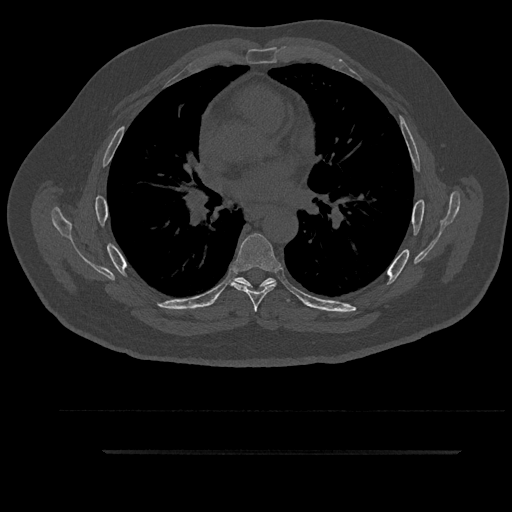
CT including the spine, one axial slice; slice 564 of 797 in the series (ordered by position); reconstruction kernel Br40s/3; 120 kVp; bone window (W 1800 / L 400 HU); 512 × 512 image matrix, field of view 432 × 432 mm. Patient: male, 63 years. Case-level facts recorded for this patient, not image findings: primary cancer: renal; vertebrae with lytic lesions (as recorded): T8.
Structures marked on this image (semi-automatic segmentation, software-assisted and operator-edited):
- T5 vertebra: bounding box [x1, y1, x2, y2] px = [235, 278, 266, 291]
- T6 vertebra: [231, 233, 280, 312]
- T7 vertebra: [234, 278, 290, 302]